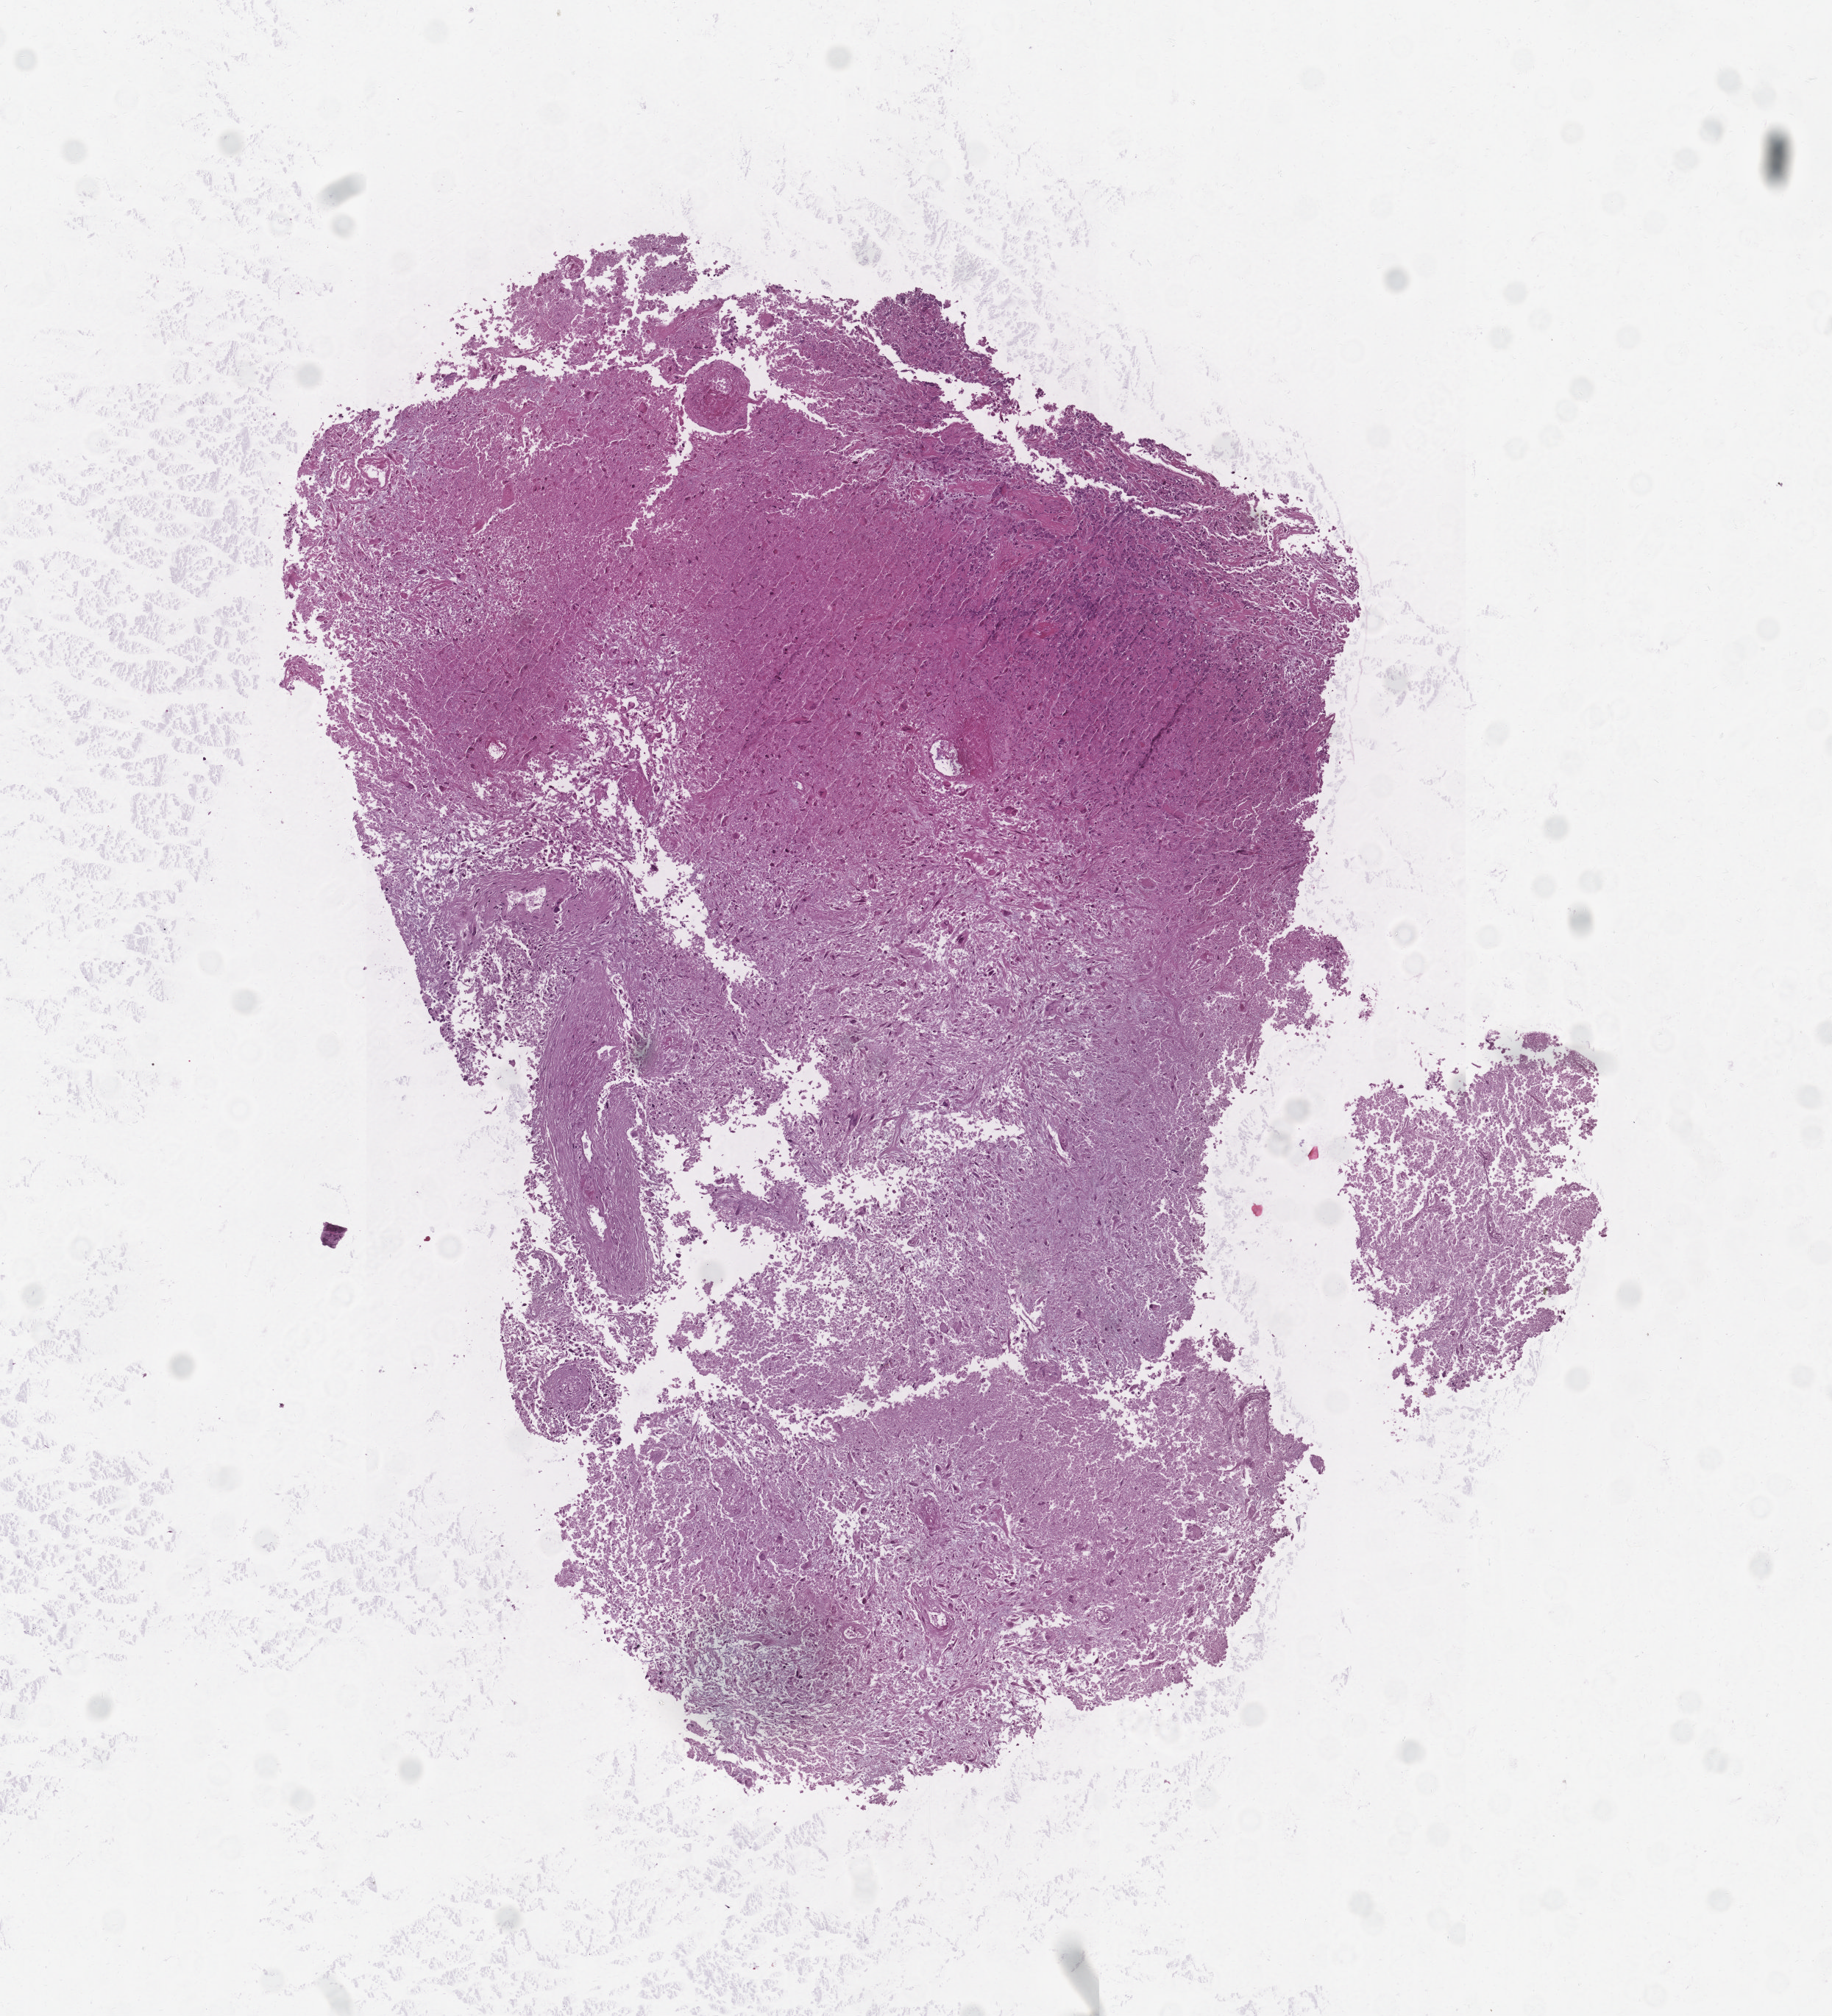
Whole-slide histology image, H&E-stained — a low-resolution overview of the entire scanned area, about 5.0 x 5.5 mm (slide scanned at 20x), tumour tissue sample, brain. Patient: male, age 59 years.
Primary tumour site (as recorded): temporal lobe. Histologic diagnosis: Glioblastoma.